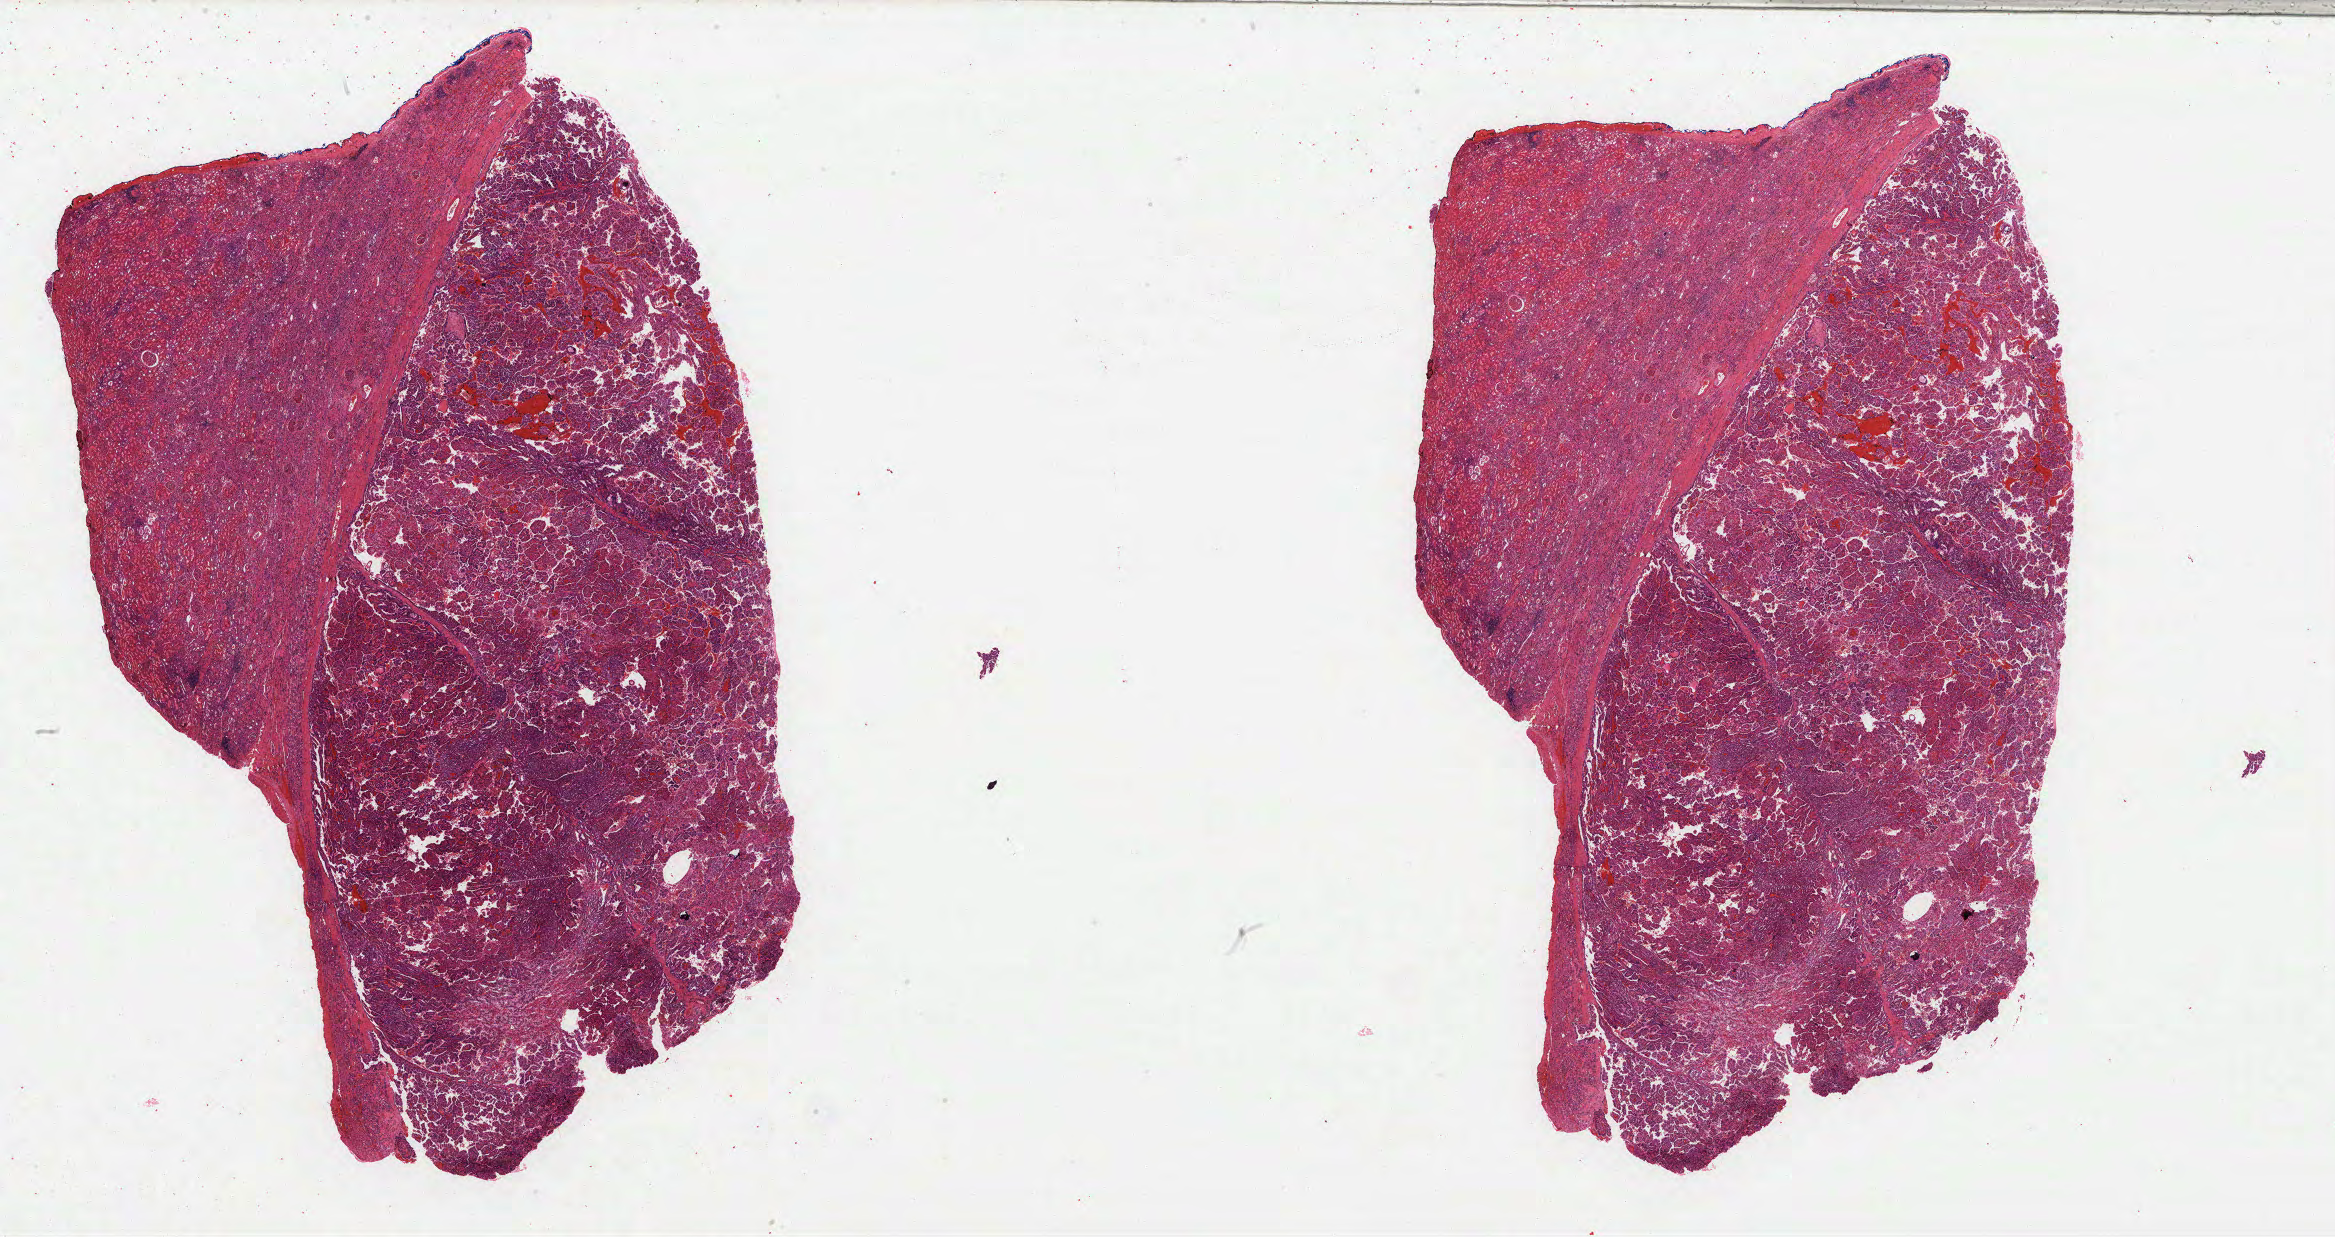
Hematoxylin and eosin (H&E) stained whole-slide image, low-resolution overview of the scanned area, about 37.1 x 19.6 mm, formalin-fixed paraffin-embedded (FFPE) diagnostic section, sample: primary tumour, kidney. Female, age 49 years at initial diagnosis.
Diagnosis: Papillary adenocarcinoma, NOS. AJCC pathologic stage: I.